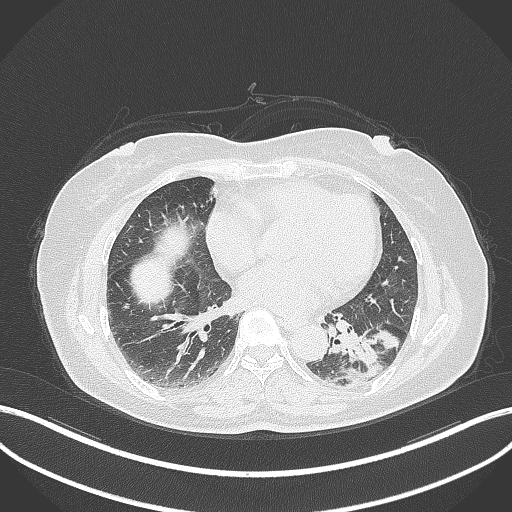
Chest CT, one axial slice; position 156 of 311 along the scan axis; reconstruction kernel B70f; lung window (W 1500 / L -600 HU); 1 mm slice thickness; 512 × 512 image matrix, field of view 400 × 400 mm. Female patient, age 59 years. Case-level facts recorded for this patient, not image findings: clinical TNM (as recorded): T2a N0 M0; histopathological grade: G2-3.
Structures marked on this image (bounding box drawn by a radiologist):
- lung tumour (recorded histology: adenocarcinoma): bounding box [x1, y1, x2, y2] px = [344, 325, 402, 389]